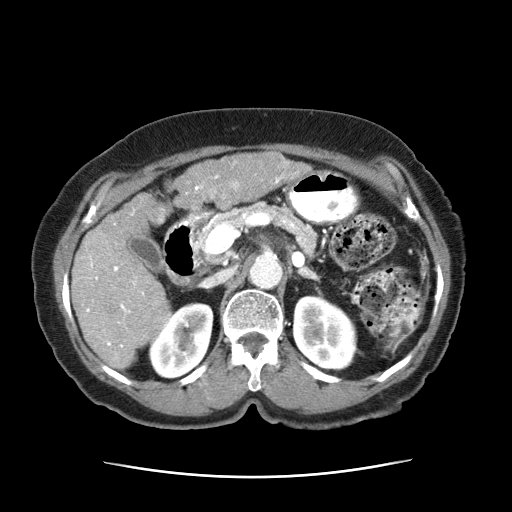
Contrast-enhanced abdominal CT (liver protocol), one axial slice. Slice 24 of 63 in the series (ordered by position). Reconstruction kernel STANDARD. Intravenous contrast given. Soft-tissue window (W 400 / L 40 HU). 2.5 mm slice thickness. 512 × 512 image matrix, field of view 360 × 360 mm. Patient: female, 79 years. From the clinical record (not read from this slice): diagnosis: hepatocellular carcinoma (patient treated with transarterial chemoembolisation; whether this scan precedes or follows treatment is not stated here); TNM stage (as recorded): Stage-II; Child-Pugh class: B; tumour differentiation: well differentiated; tumour nodularity: multinodular.
Annotated regions visible in this slice (semi-automatically segmented with operator editing):
- abdominal aorta: box from (x=249, y=251) to (x=282, y=288) px
- liver parenchyma outside the tumour (the mass and vessels are separate outlines, so this box may not span the whole liver): (x=72, y=192)–(x=173, y=372)
- mass: (x=178, y=152)–(x=310, y=208)
- liver vessels: (x=82, y=174)–(x=284, y=348)